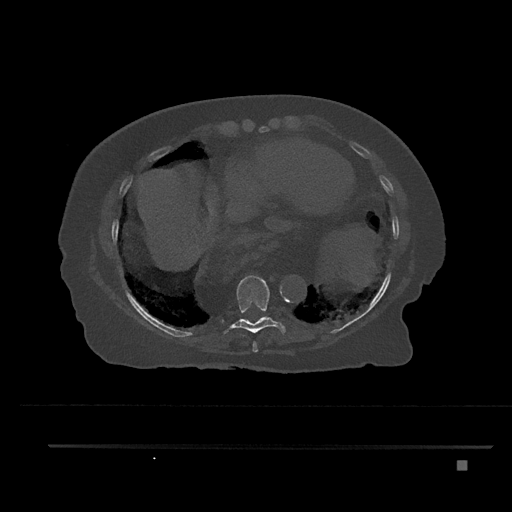
CT including the spine, one axial slice. Slice 399 of 797 in the series (ordered by position). Reconstruction kernel Br40s/3. 120 kVp. Bone window (W 1800 / L 400 HU). 512 × 512 image matrix, field of view 437 × 437 mm. Patient: female, 76 years. Case-level facts recorded for this patient, not image findings: primary cancer: lung; vertebrae with lytic lesions (as recorded): T11, L3.
Annotated regions visible in this slice (semi-automatic segmentation, software-assisted and operator-edited):
- T8 vertebra: bounding box [x1, y1, x2, y2] px = [252, 341, 258, 352]
- T9 vertebra: [222, 276, 286, 335]